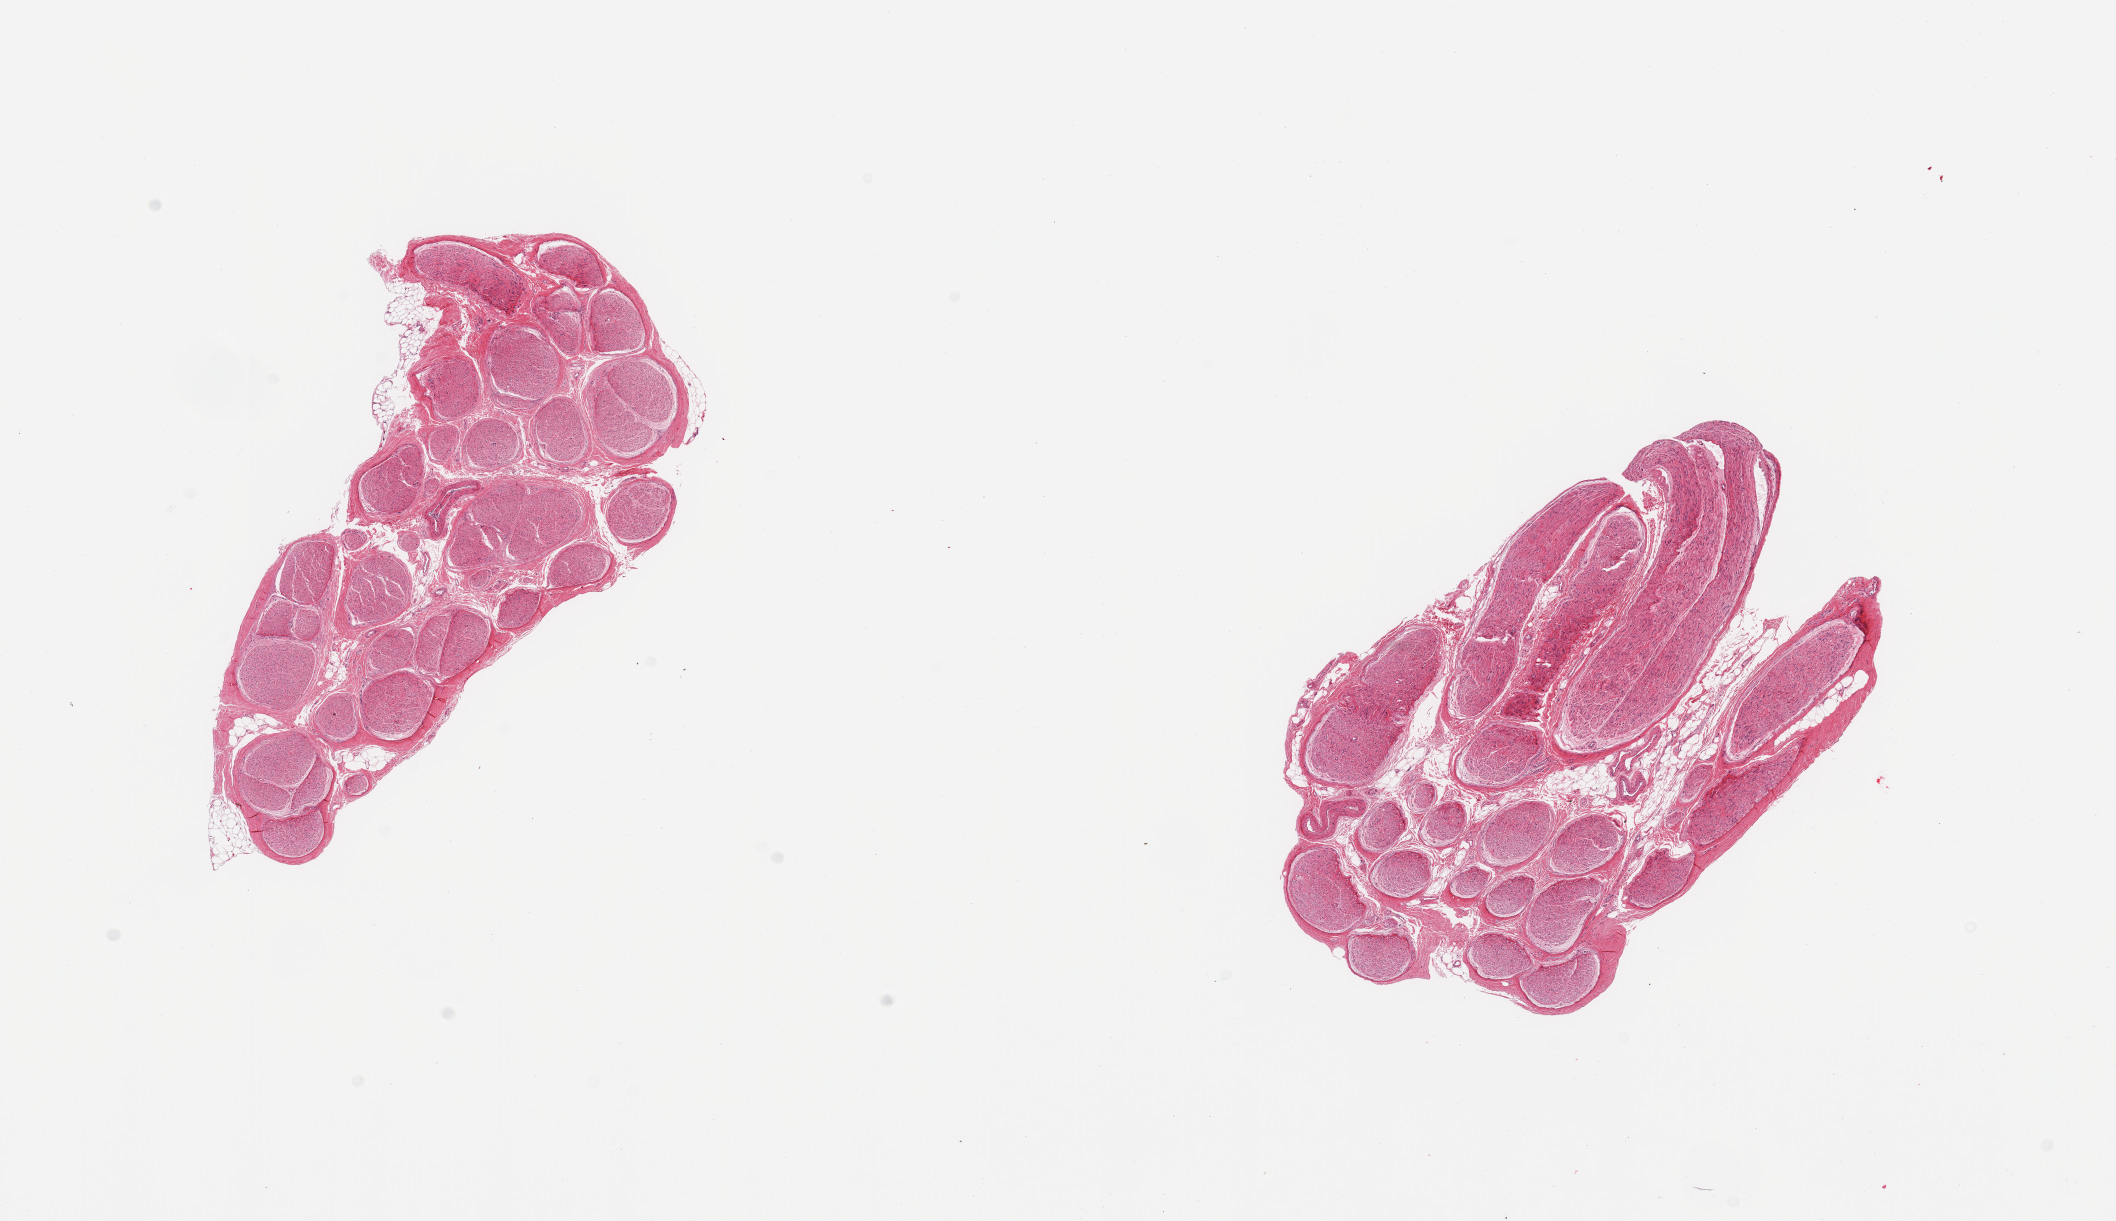
Digitized haematoxylin and eosin-stained section, brightfield, whole scanned area (about 16.7 x 9.7 mm) shown as a low-resolution overview, PAXgene-fixed paraffin-embedded (PFPE) section, target tissue: tibial nerve, donor tissue sample. Donor sex: male.
Reviewer comment on this tissue sample: 2 pieces, no significant adherant fat.